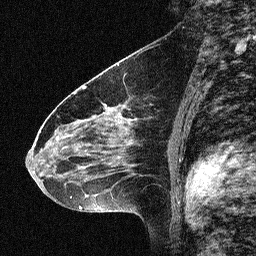
Breast MRI (dynamic contrast-enhanced), one sagittal slice. Slice 35 of 64 in the series (ordered by position). Dynamic contrast-enhanced study with each time point stored as its own series, time point 2 of 3 at this slice position (early post-contrast, ordered by acquisition time). 1.5 T. TE 4.5 ms, TR 11 ms. 2.06 mm slice thickness. 256 × 256 image matrix. Patient: female, 46 years. Case-level facts recorded for this patient, not image findings: setting: breast cancer imaged before/during neoadjuvant chemotherapy; receptor status: HER2-positive.
Annotated regions visible in this slice (semi-automatic segmentation, software-assisted and operator-edited):
- analysis volume of interest (the breast-tissue region the enhancement analysis was run in; not a lesion): bounding box (x1, y1, x2, y2) in pixels: (42, 80, 150, 180)
- tumour enhancement mask (voxels above the 90 % enhancement threshold inside the analysis volume of interest): (46, 105, 106, 144)